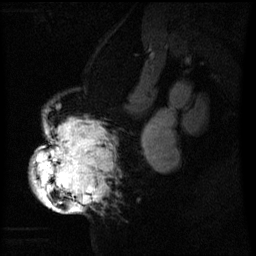
Breast MRI (dynamic contrast-enhanced), one sagittal slice. Position 36 of 60 along the scan axis. Dynamic contrast-enhanced series, image 2 of 3 at this slice position (ordered by acquisition). 1.5 T. TE 4.2 ms, TR 8 ms. 2.2 mm slice thickness. 256 × 256 image matrix, field of view 200 × 200 mm. Female patient, age 50 years.
Structures marked on this image (semi-automatic segmentation, software-assisted and operator-edited):
- analysis volume of interest (the breast-tissue region the enhancement analysis was run in; not a lesion): bounding box [x1, y1, x2, y2] px = [32, 118, 111, 211]
- tumour enhancement mask (voxels above the 70 % enhancement threshold inside the analysis volume of interest): [33, 120, 106, 211]